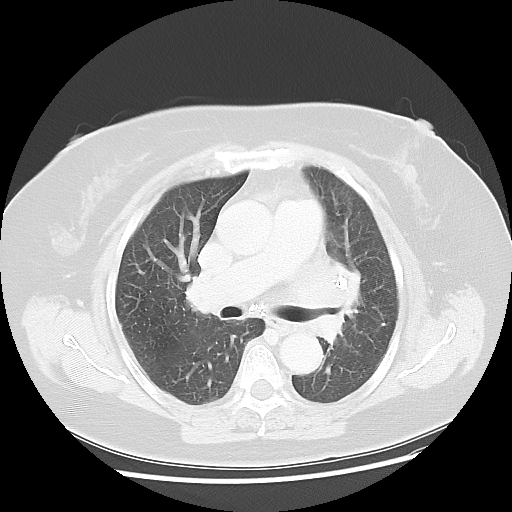
Chest CT, one axial slice. Slice 27 of 49 in the series (ordered by position). 120 kVp. Lung window (W 1500 / L -600 HU). 5 mm slice thickness. 512 × 512 image matrix. Female patient, age 58 years. Case-level facts recorded for this patient, not image findings: clinical TNM (as recorded): T4 N3 M0; histopathological grade: G3.
Structures marked on this image (rectangle marked by the reading radiologist):
- lung tumour (recorded histology: small cell carcinoma): bounding box <310,239,362,358> (left, top, right, bottom; pixels)